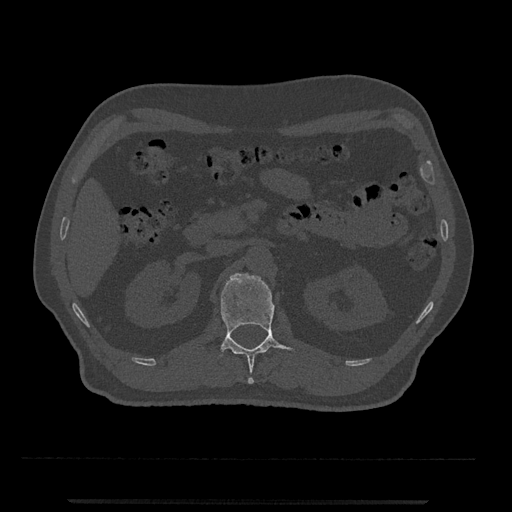
CT including the spine, one axial slice. Slice 330 of 797 in the series (ordered by position). Reconstruction kernel Br40s/3. 120 kVp. Bone window (W 1800 / L 400 HU). 0.5 mm slice thickness. 512 × 512 image matrix. Patient: male, 63 years. Case-level facts recorded for this patient, not image findings: primary cancer: prostate.
Structures marked on this image (semi-automatic segmentation, software-assisted and operator-edited):
- L1 vertebra: bounding box [x1, y1, x2, y2] px = [218, 273, 295, 384]